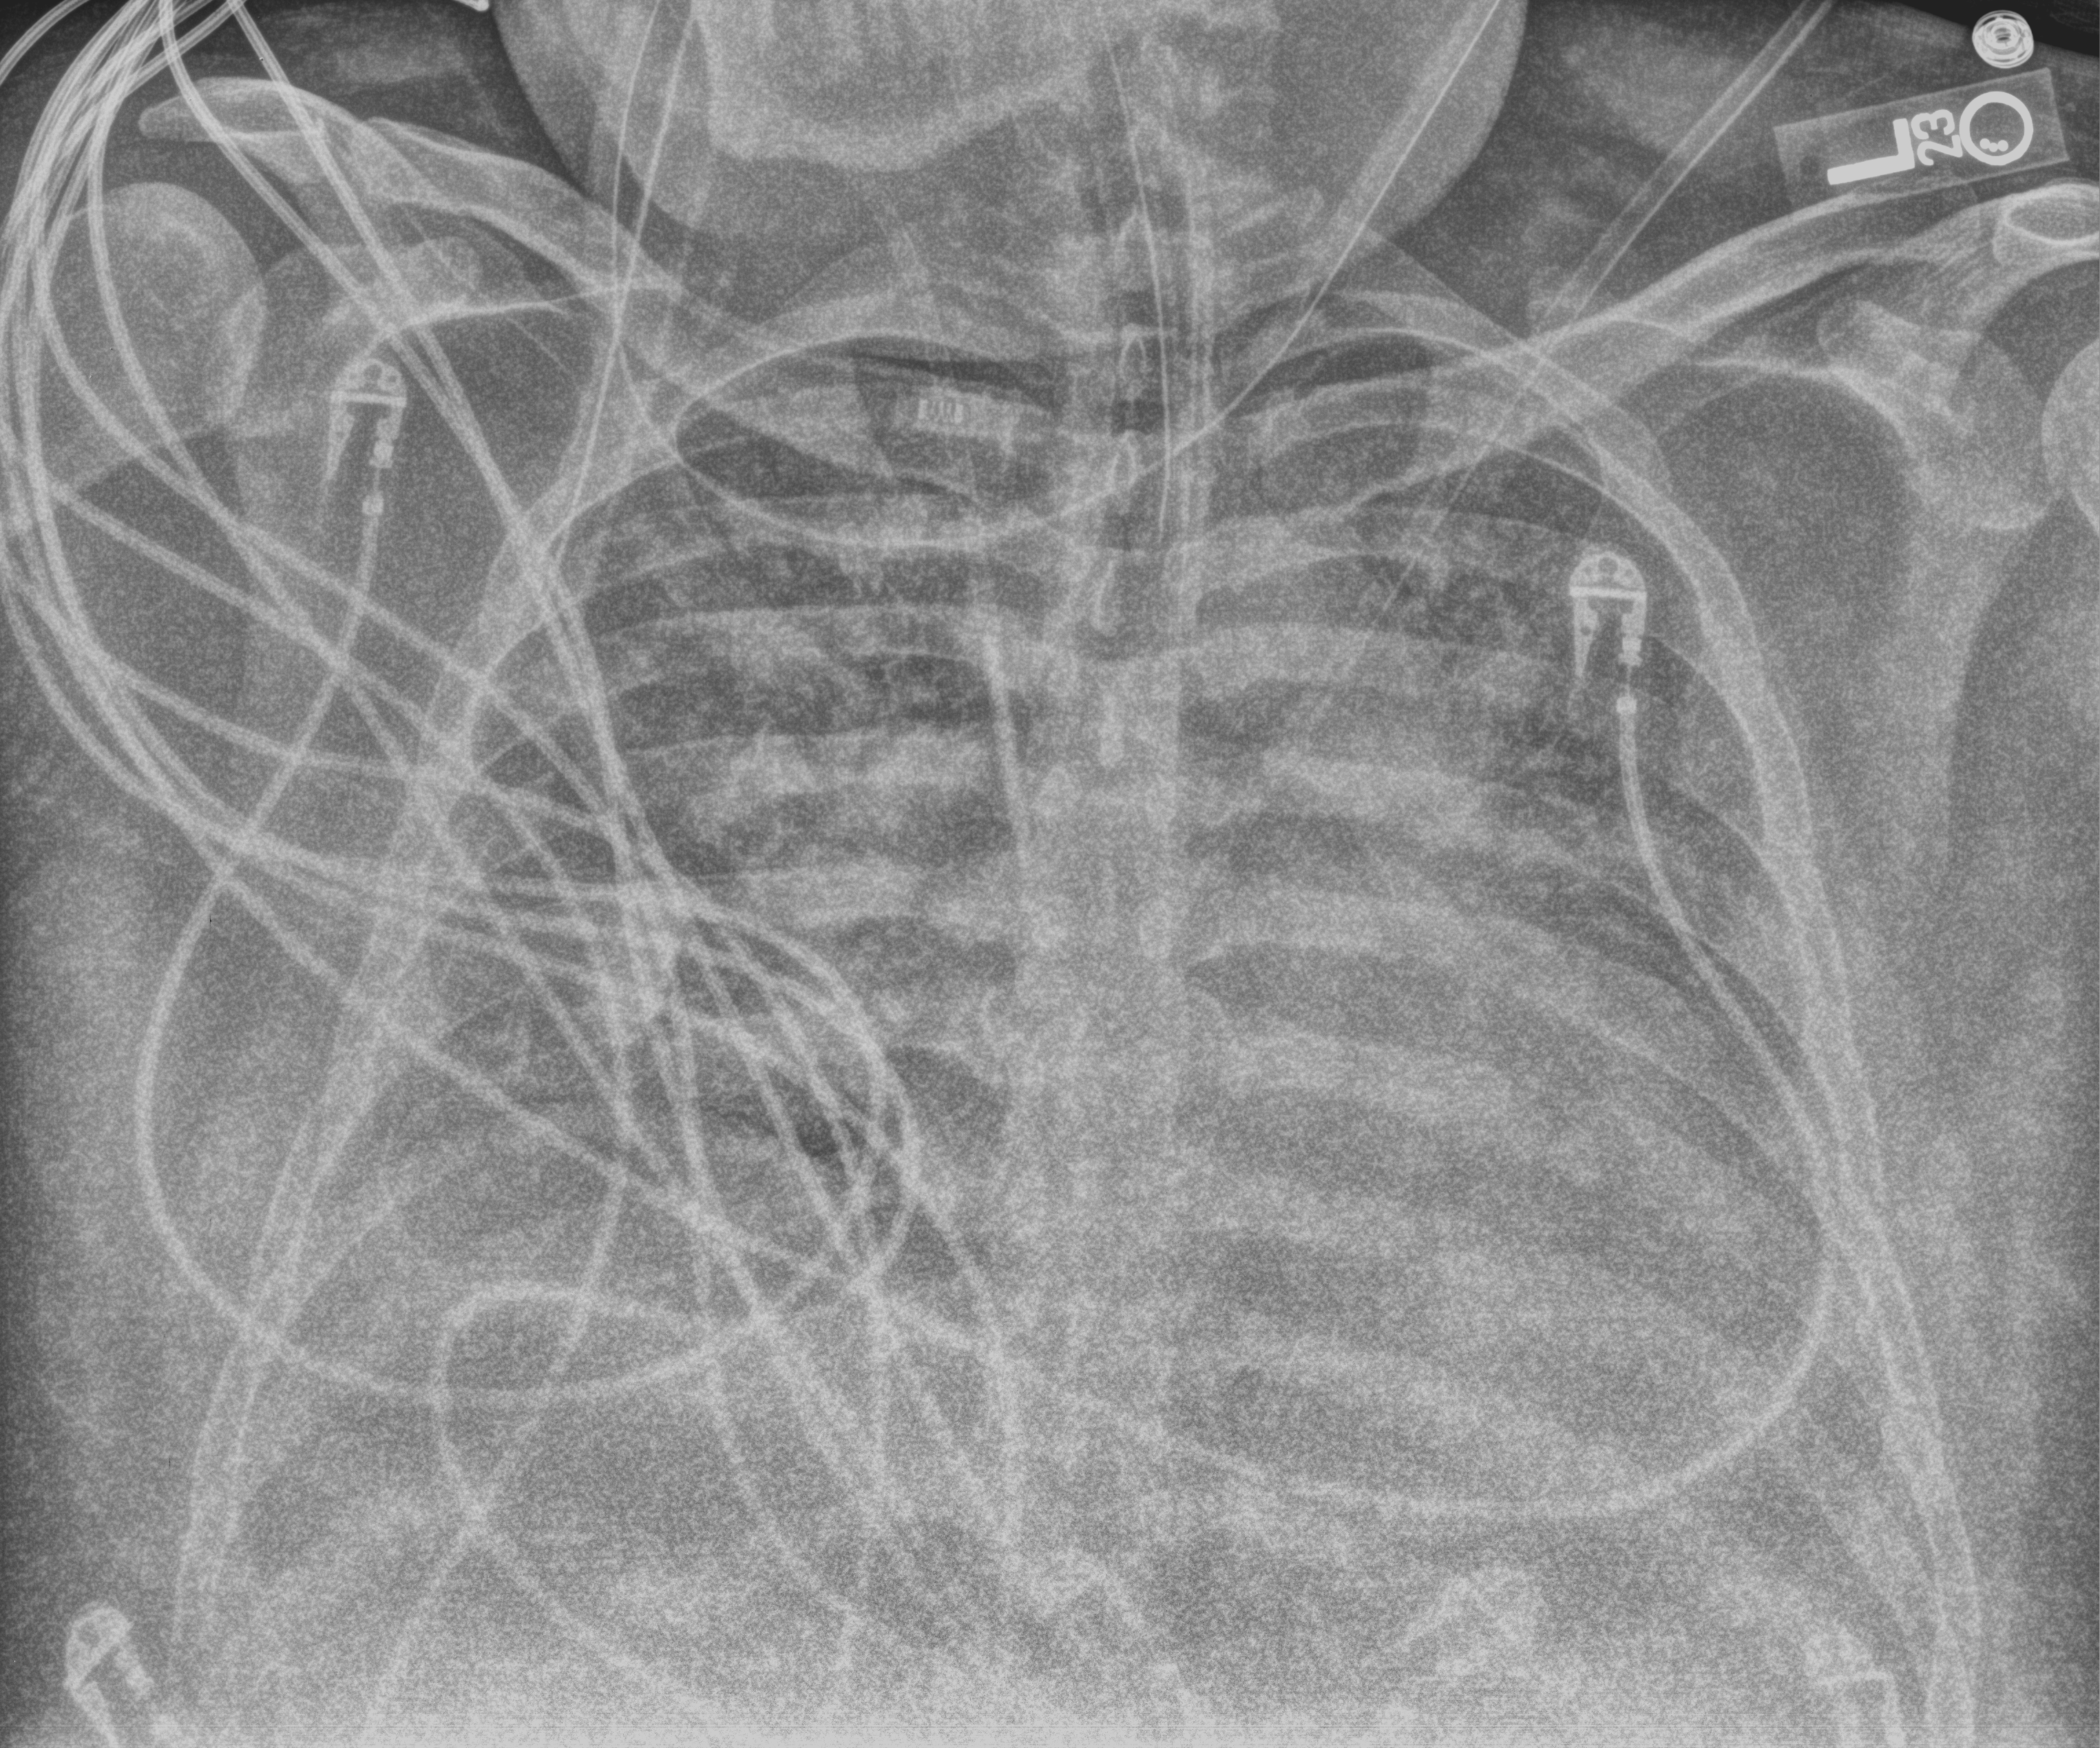
Portable chest radiograph, anteroposterior (AP) projection. Adult patient hospitalised with COVID-19, age 18–59 years.
Admission-level facts for this patient (not findings on this image; timing relative to this image not recorded):
- mechanically ventilated during this hospital stay: yes
- smoking status (admission record): former
- admitted to intensive care during this hospital stay: yes